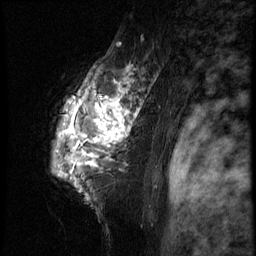
Breast MRI (dynamic contrast-enhanced), one sagittal slice; position 54 of 66 along the scan axis; 3 images stored at this slice position (order not interpretable as contrast timing); 1.5 T; TE 4.2 ms, TR 8.9 ms; 256 × 256 image matrix. Female patient, age 39 years. From the clinical record (not read from this slice): setting: breast cancer imaged before/during neoadjuvant chemotherapy; receptor status: HER2-positive.
Outlined on this slice (semi-automatically segmented with operator editing):
- analysis volume of interest (the breast-tissue region the enhancement analysis was run in; not a lesion): bounding box <48,44,166,196> (left, top, right, bottom; pixels)
- tumour enhancement mask (voxels above the 140 % enhancement threshold inside the analysis volume of interest): <58,67,143,172>